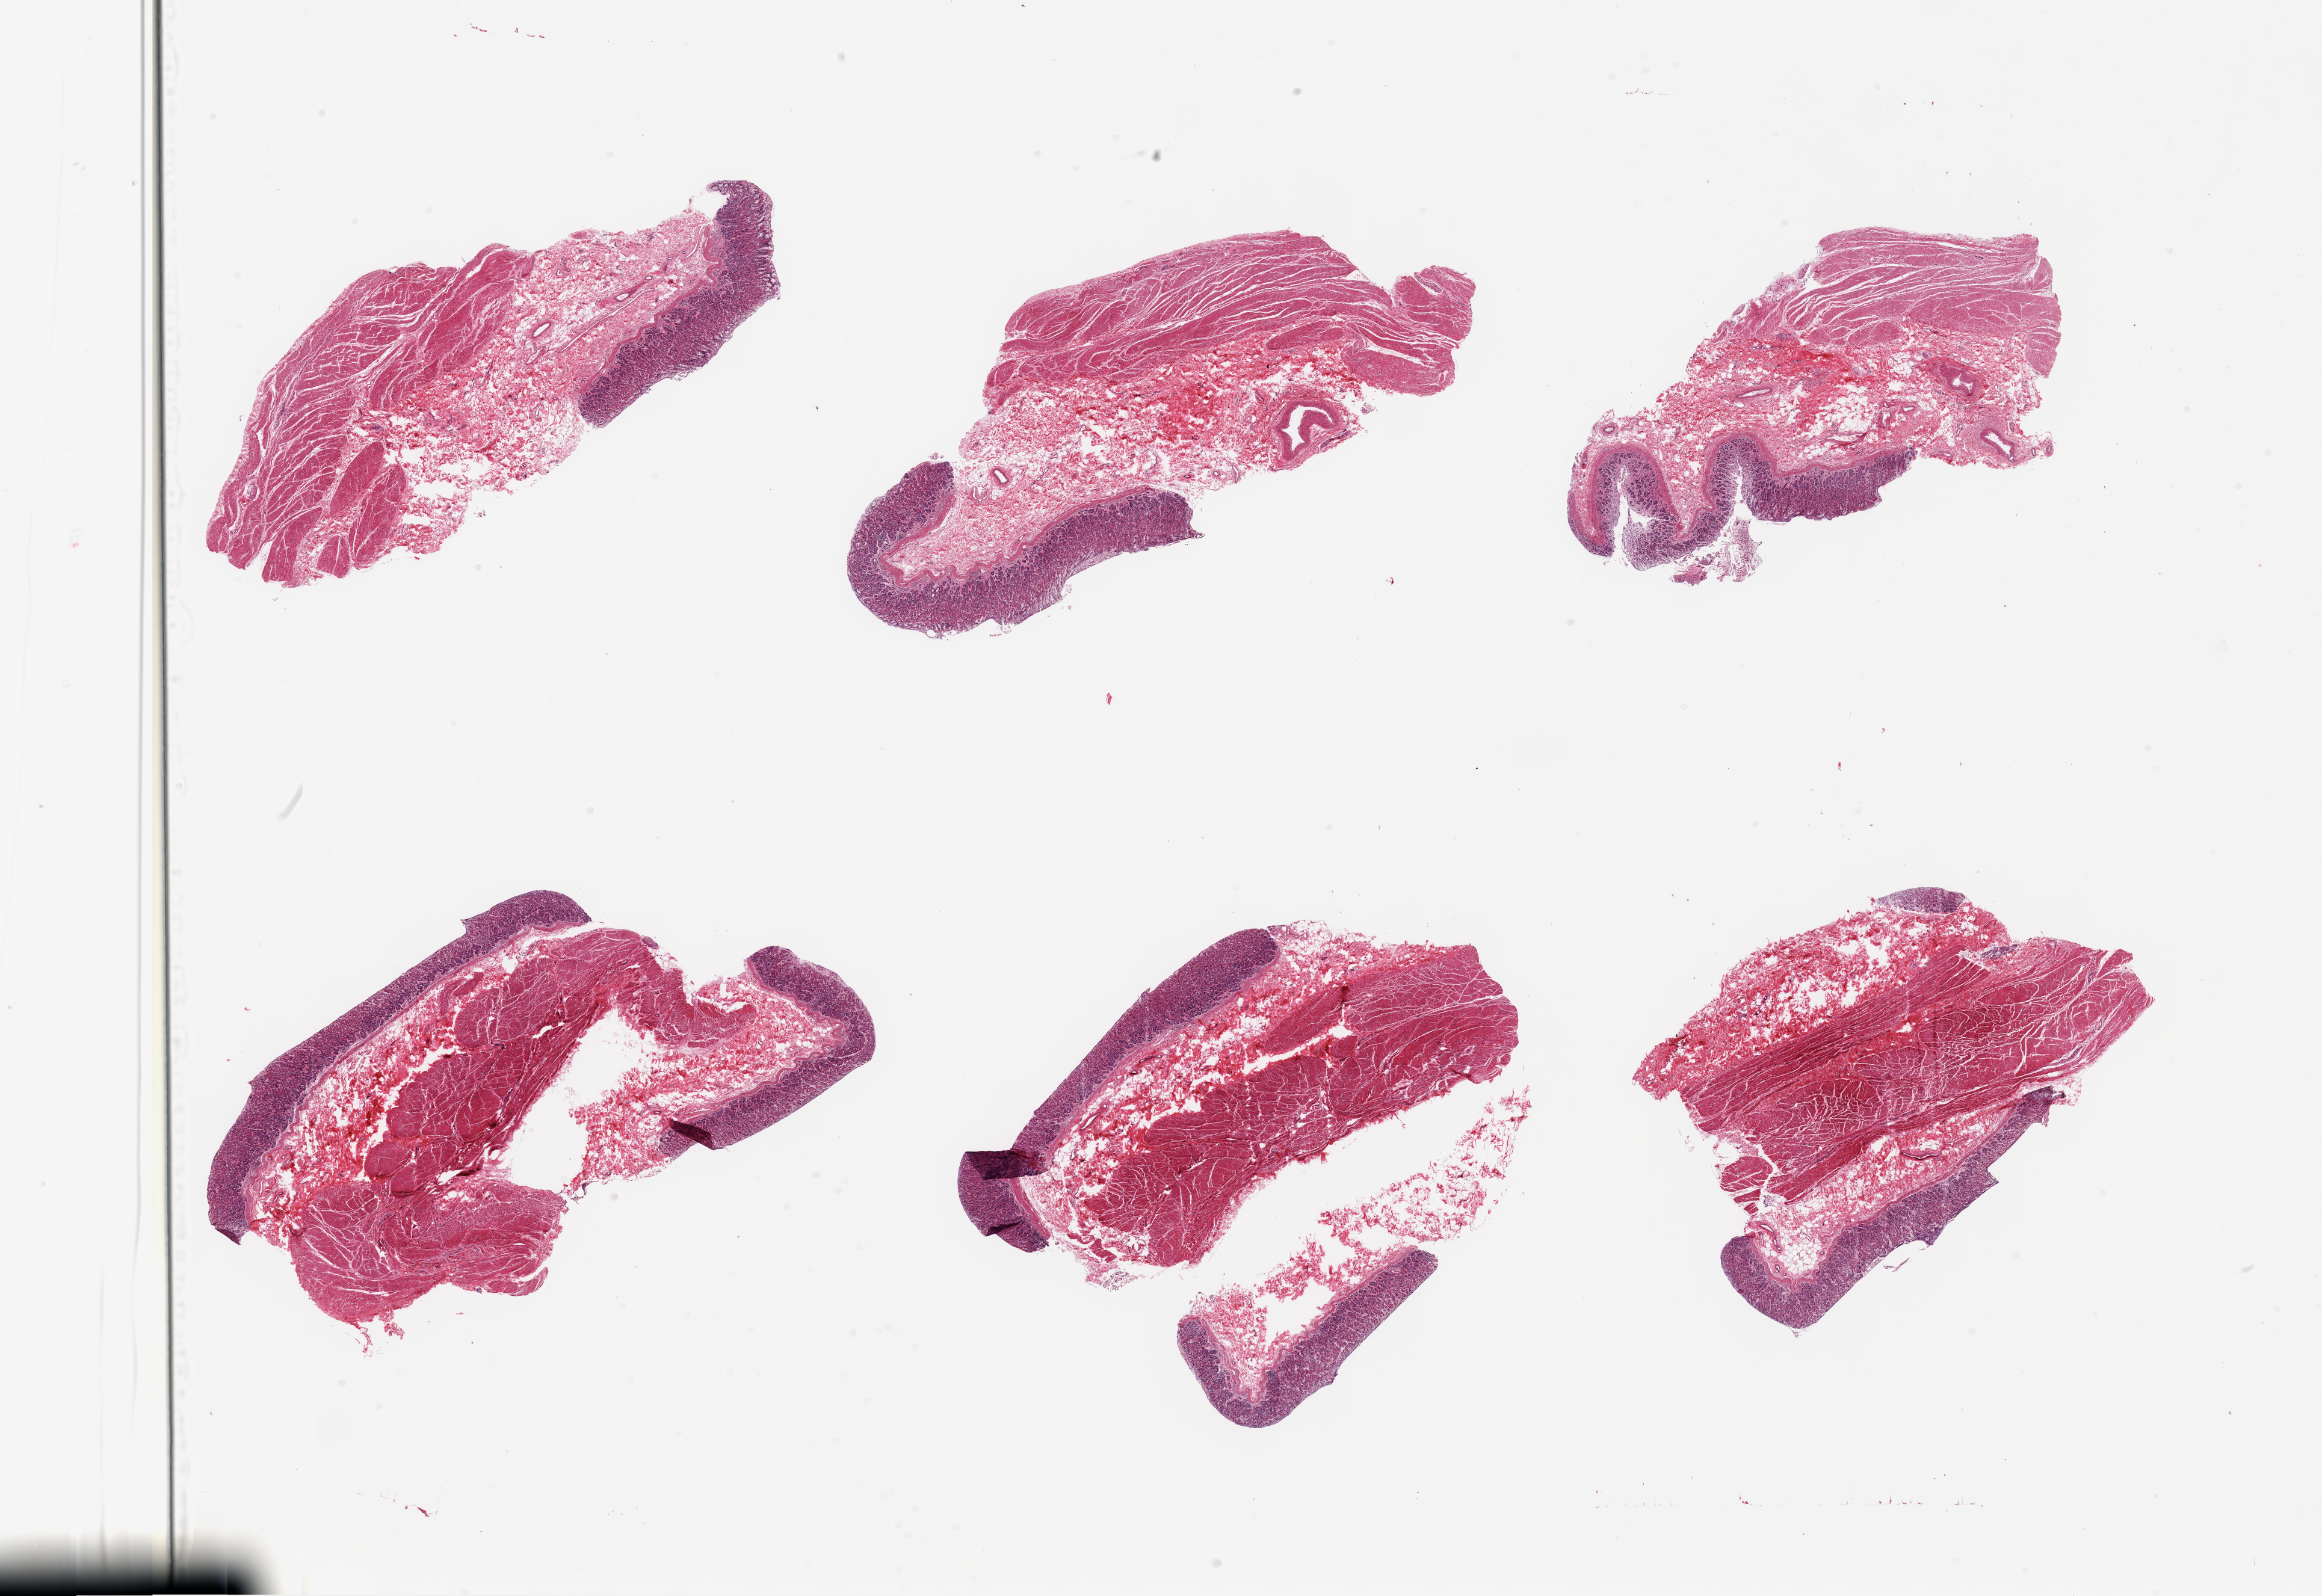
Digitized H&E-stained section — low-resolution overview of the scanned area, about 30.5 x 21.0 mm (from a 20x scan). PAXgene-fixed paraffin-embedded (PFPE) section. Target tissue: stomach. Tissue donor sample. Donor: male.
* pathologist's review note for this sample: 6 pieces, mucosa up to ~0.8mm, 20-30% thickness